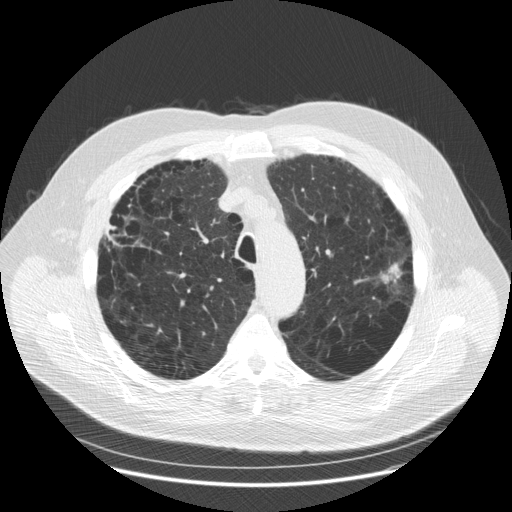
Axial slice from a low-dose chest CT screening exam, first (baseline) screen, lung window (W 1500 / L -600 HU), 2.5 mm slice thickness, slice 46 of 179 in the series. Male, age 70 years at enrolment. Current smoker at enrolment.
- Expert-annotated lung lesion, bounding box (x1, y1, x2, y2) in pixels: (362, 247, 419, 298).
- The exam's reader record, not a measurement of the box and not confirmed to be the same lesion: non-calcified nodule or mass ≥4 mm, left upper lobe, 25 × 13 mm, spiculated (stellate) margins, soft tissue attenuation.
- Participant outcome: lung cancer diagnosed 62 days after this screen — adenocarcinoma, NOS, left upper lobe, moderately differentiated (G2), stage IA (AJCC 6th edition), 22 mm at pathology.